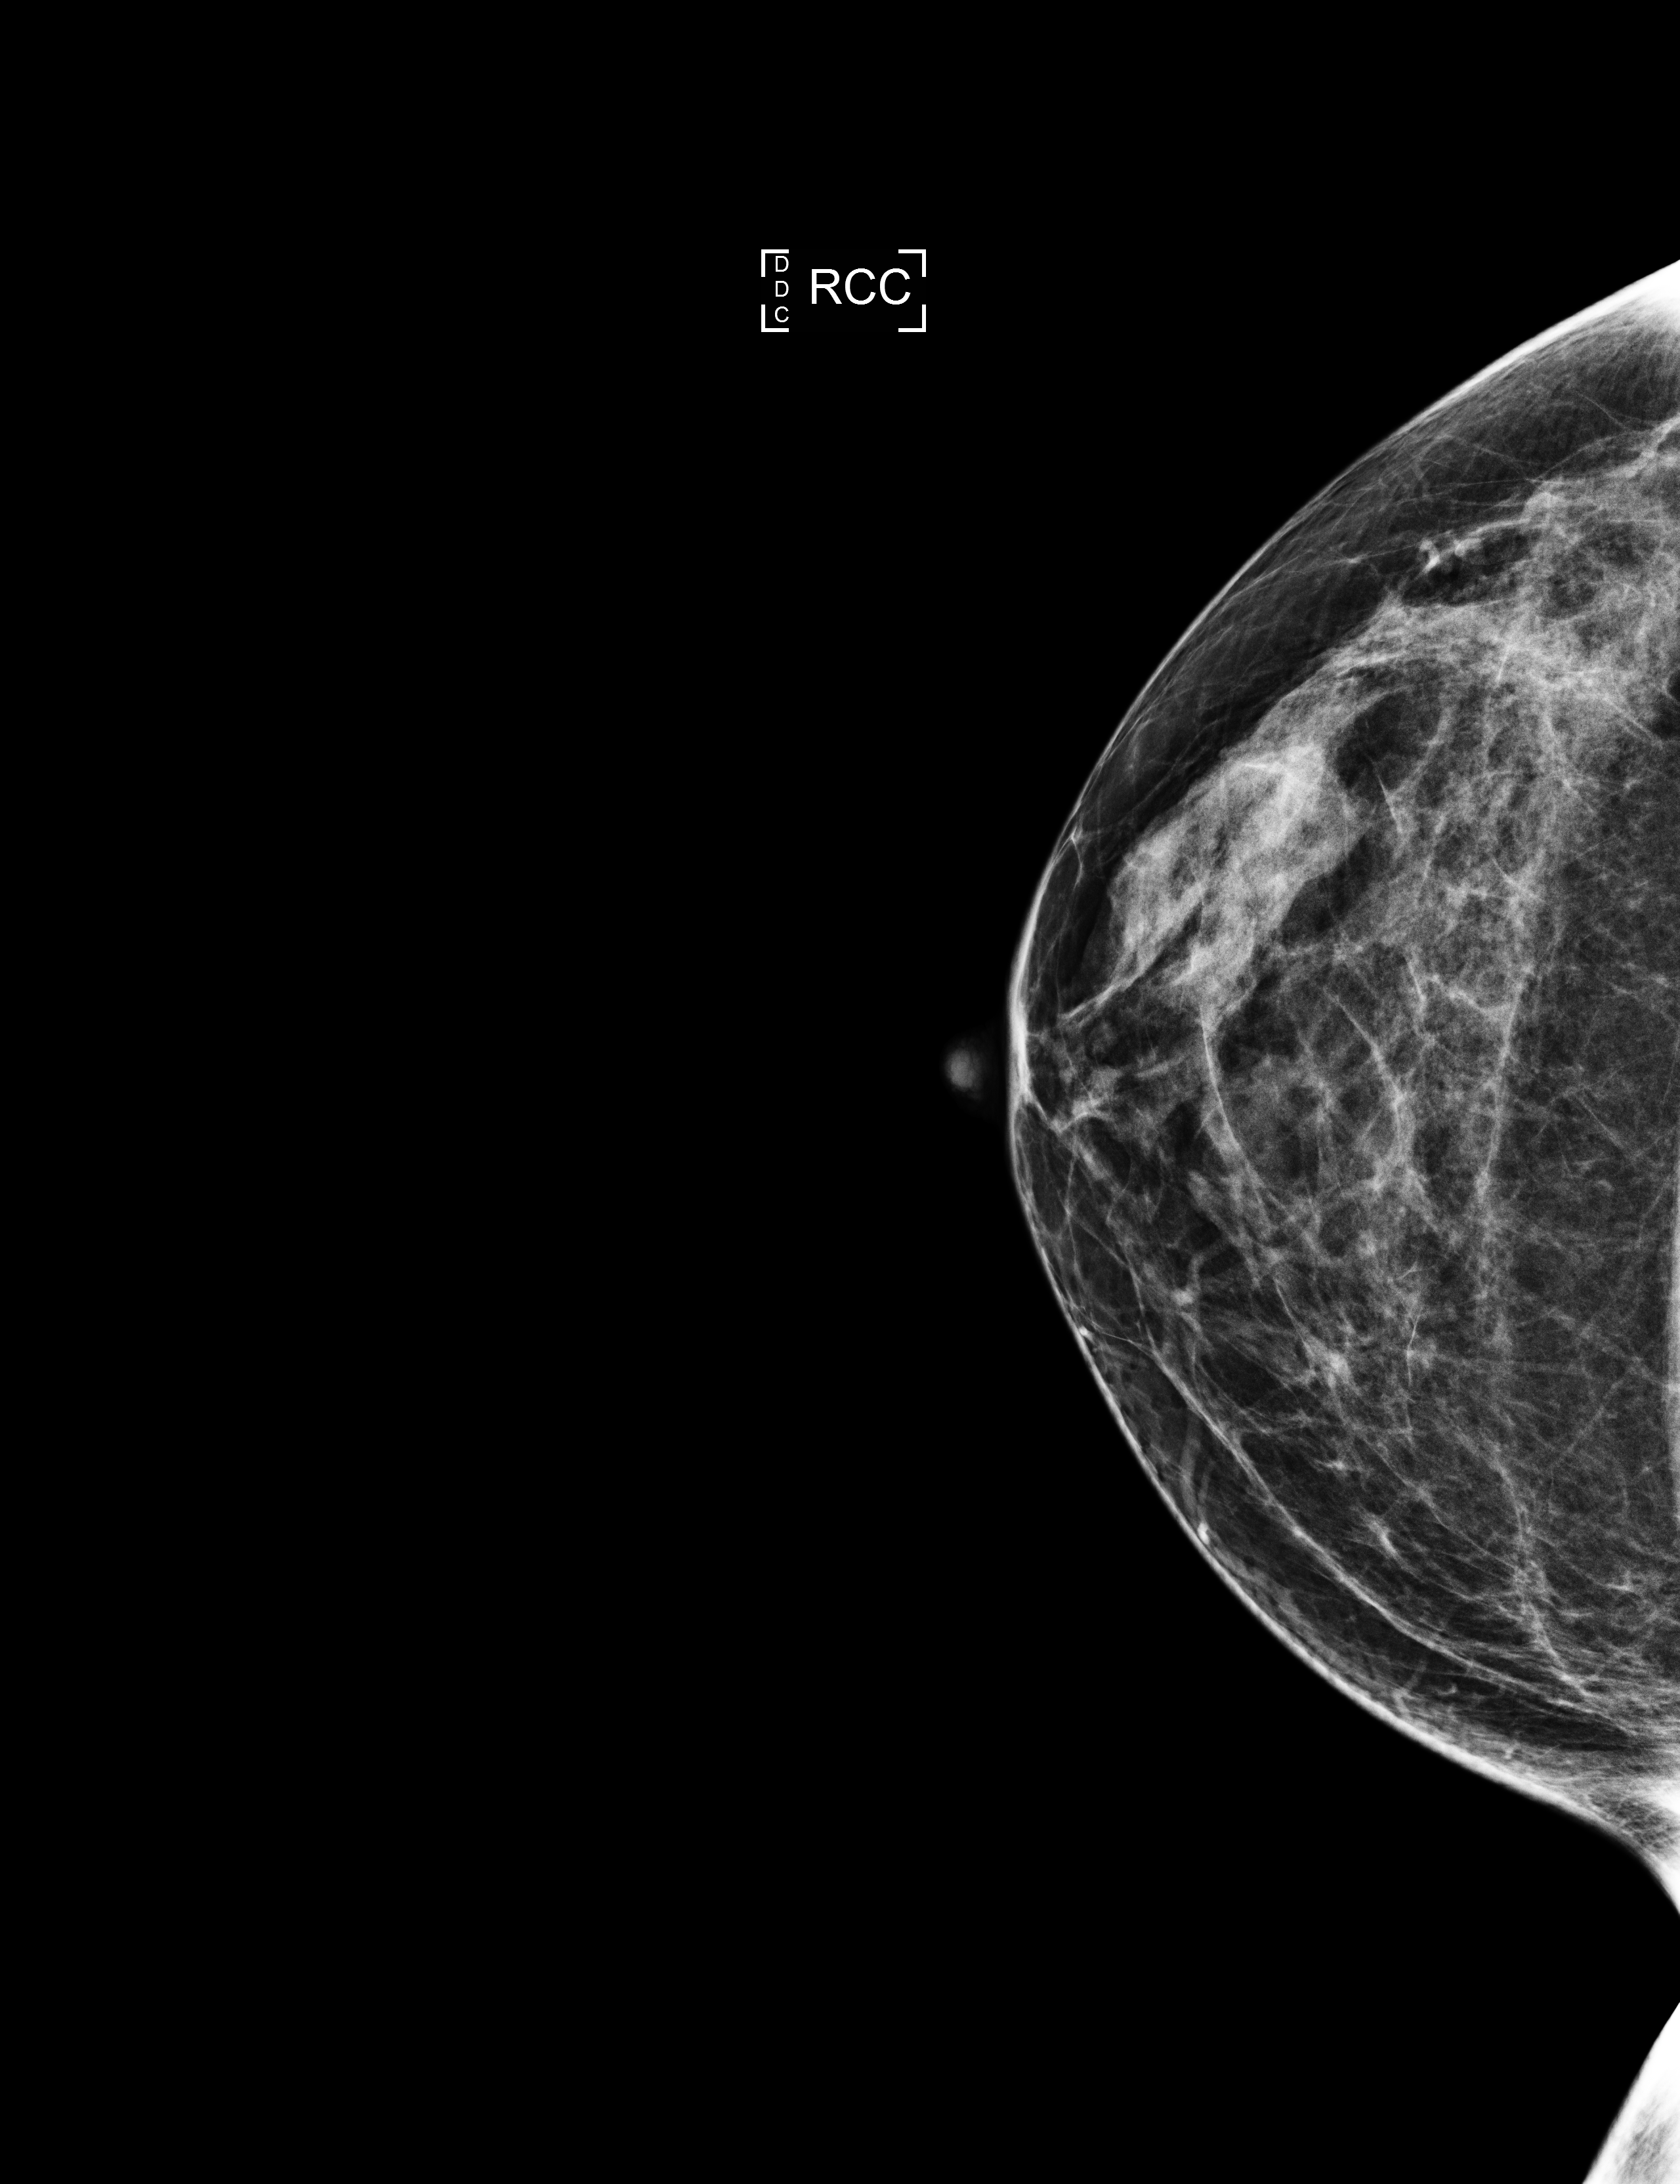
Annual screening mammography examination. Female patient, age 59 years.
Image type: full-field digital mammogram. Breast: right. Projection: CC view. BI-RADS breast density category at the screening exam (both breasts, scale 1–4): 3. Final BI-RADS assessment for this screening round (tomosynthesis exam, both breasts): category 2. Recall: no recall after this screen.